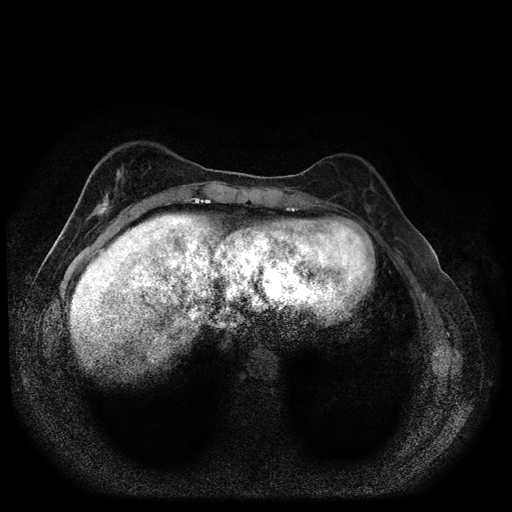
Breast MRI (dynamic contrast-enhanced, multi-phase), one axial slice; dynamic contrast-enhanced series, time point 2 of 5 at this slice position (early post-contrast); 1.5 T; TE 2.7 ms, TR 5.4 ms; 2 mm slice thickness; 512 × 512 image matrix, field of view 330 × 330 mm. Female patient, age 49 years.
Structures marked on this image (semi-automatic segmentation, software-assisted and operator-edited):
- breast lesion (labelled 'tumour' in the annotation; benign lesions carry a separate 'benign' label): box from (x=84, y=166) to (x=128, y=225) px